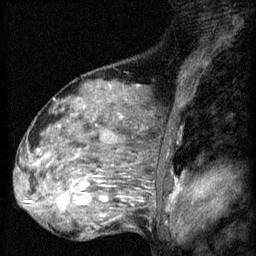
Breast MRI (dynamic contrast-enhanced), one sagittal slice. Position 40 of 60 along the scan axis. 3 images stored at this slice position (order not interpretable as contrast timing). 1.5 T. TE 4.2 ms, TR 8.2 ms. 2 mm slice thickness. 256 × 256 image matrix, field of view 180 × 180 mm. Patient: female, 48 years.
Outlined on this slice (semi-automatic segmentation, software-assisted and operator-edited):
- analysis volume of interest (the breast-tissue region the enhancement analysis was run in; not a lesion): bounding box <48,160,125,217> (left, top, right, bottom; pixels)
- tumour enhancement mask (voxels above the 70 % enhancement threshold inside the analysis volume of interest): <57,182,108,207>